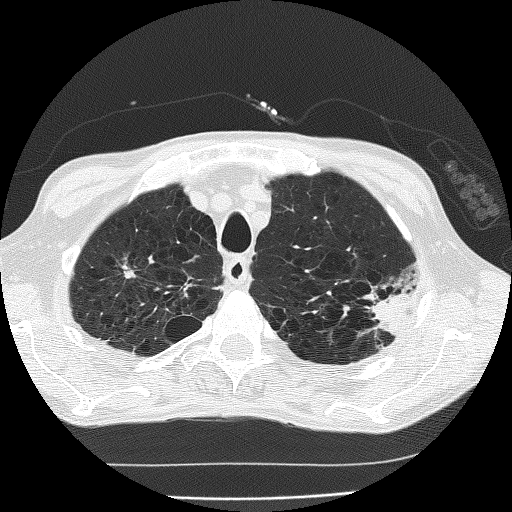
Low-dose screening chest CT, axial slice. Second annual screen. Lung window (W 1500 / L -600 HU). 2 mm slice thickness. Lung (sharp) reconstruction kernel (FC51). Slice 32 of 185 in the series. 512 × 512 image matrix. Male participant, aged 60 years at enrolment. Current smoker at enrolment.
- Expert-annotated lung lesion, bounding box <346,273,419,342> (left, top, right, bottom; pixels).
- The screening reader recorded 2 non-calcified nodules or masses ≥4 mm on this exam (left upper lobe, left upper lobe); which of them this box marks is not recorded.
- Lung cancer was diagnosed 178 days after this screen: bronchiolo-alveolar carcinoma, mucinous, left upper lobe, stage IV (AJCC 6th edition).